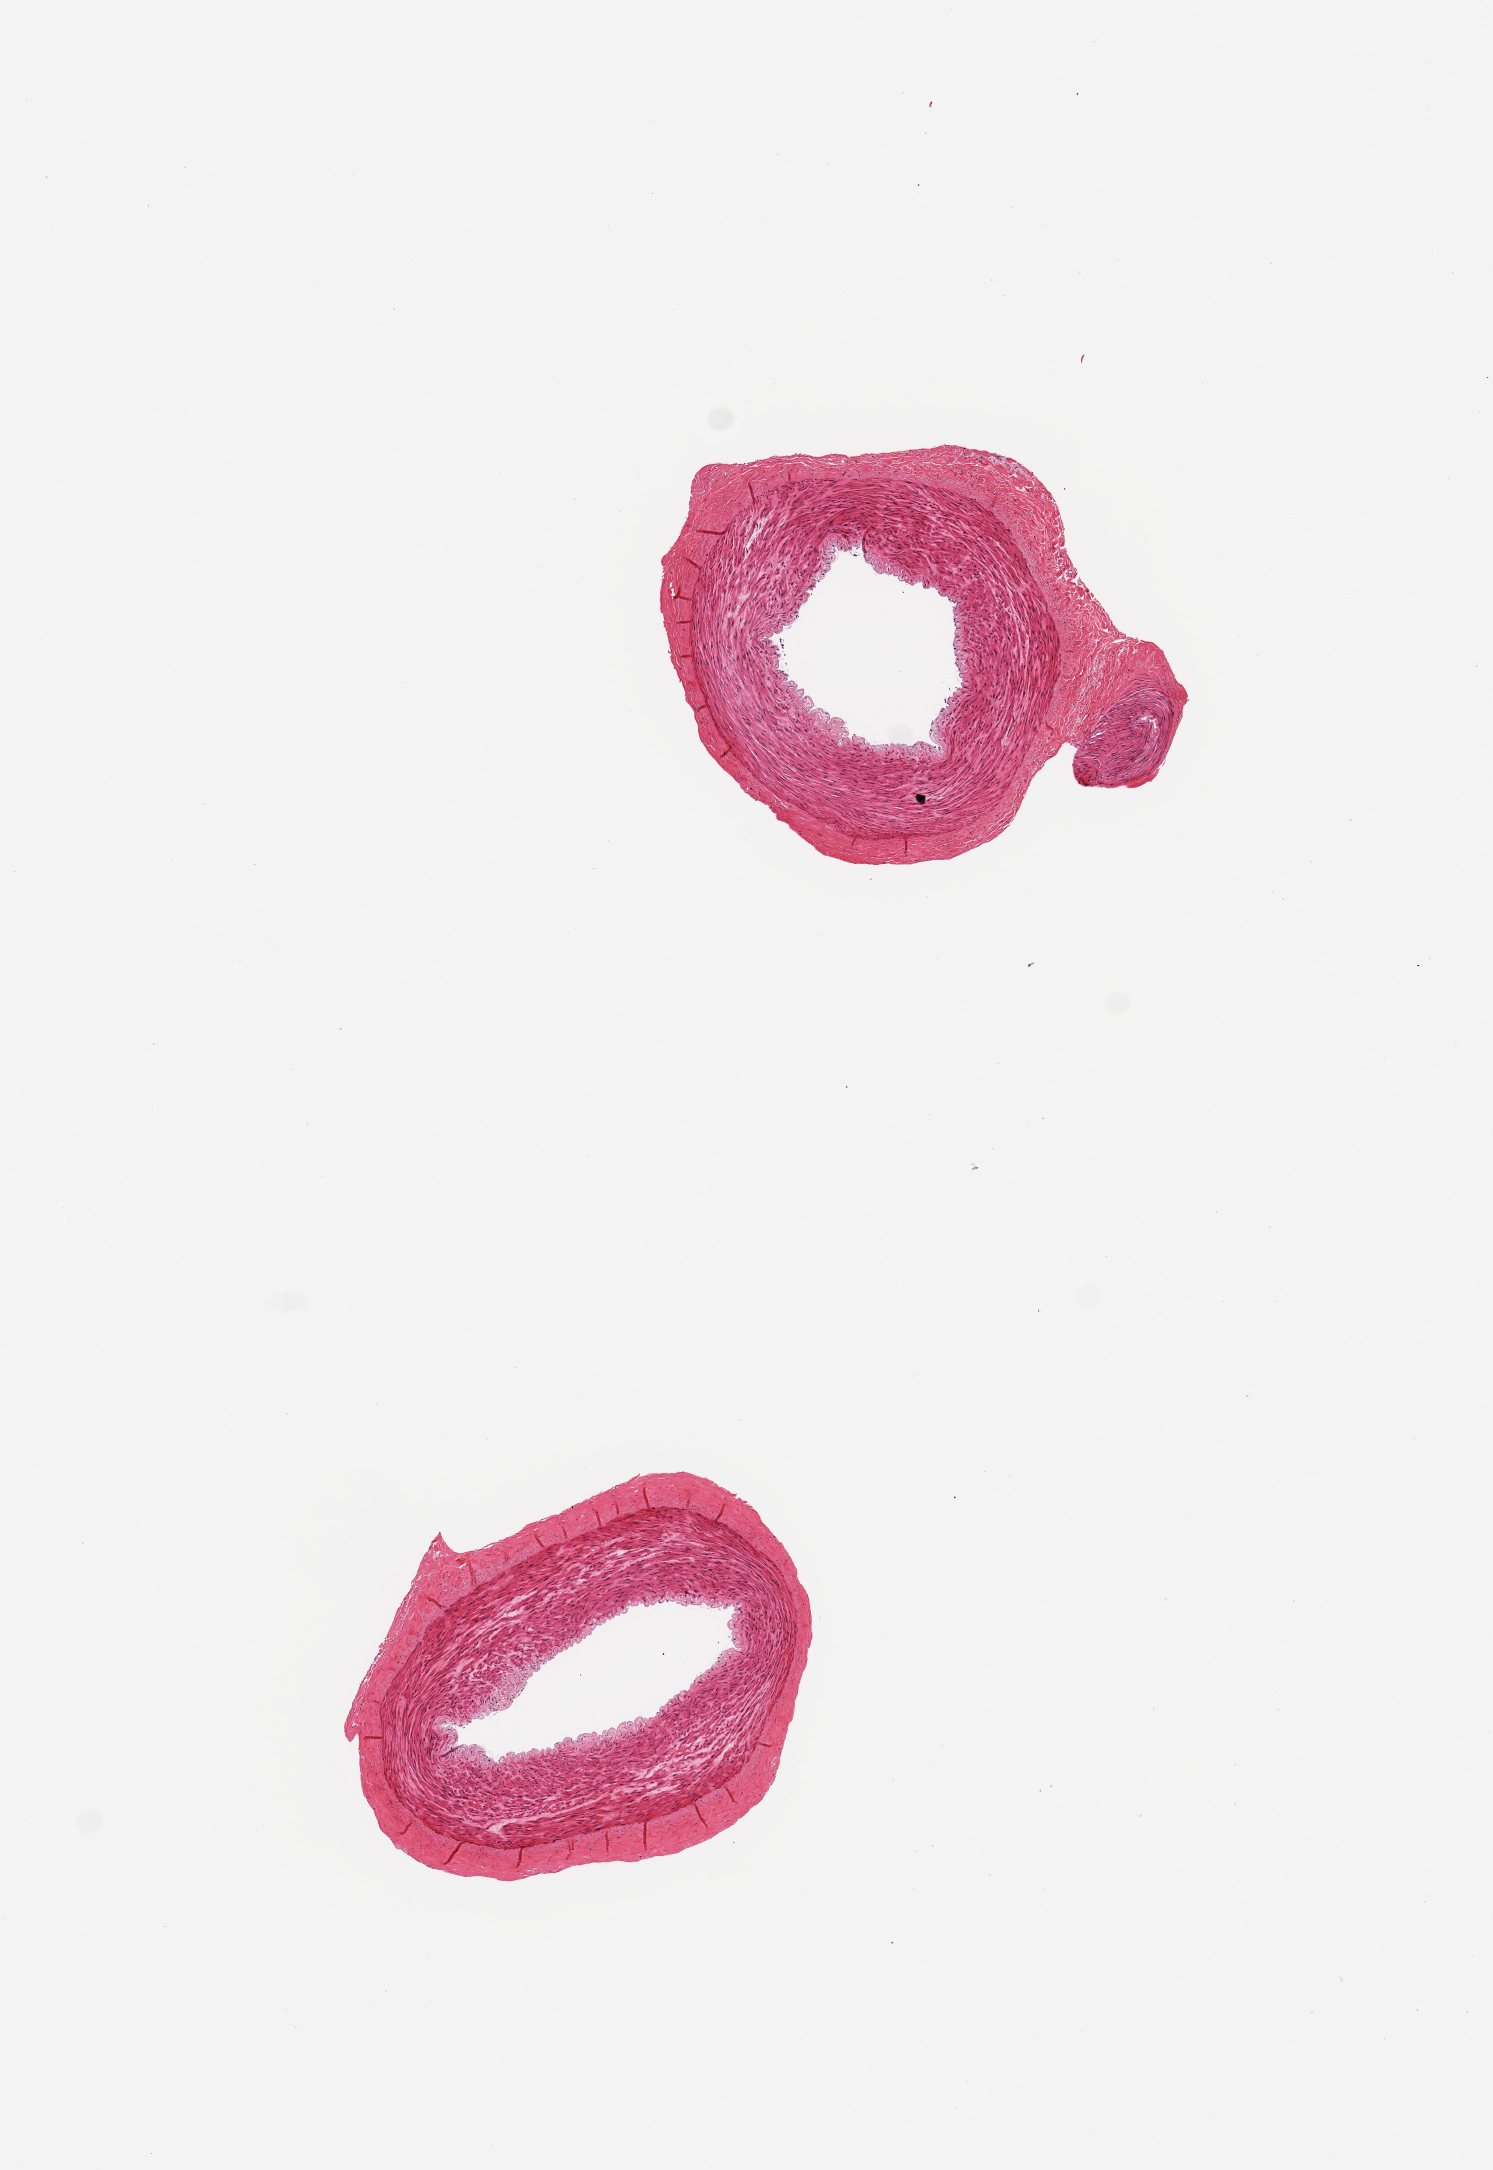
H&E whole-slide image — a low-resolution overview of the entire scanned area, about 5.9 x 8.6 mm, PAXgene-fixed paraffin-embedded (PFPE) section, target tissue: tibial artery, donor tissue sample.
Pathologist's review note for this sample: 2 pieces, no significant adherent fat/atherosis.